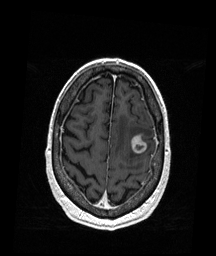
Brain MRI from a brain-tumour surgery series, one axial slice. T1-weighted post-contrast. 1 mm slice thickness. 216 × 256 image matrix, field of view 211 × 250 mm. Case-level facts recorded for this patient, not image findings: histopathology: Metastatic Melanoma.
Outlined on this slice (outlined manually by an expert reader):
- tumour: bounding box <130,132,147,153> (left, top, right, bottom; pixels)